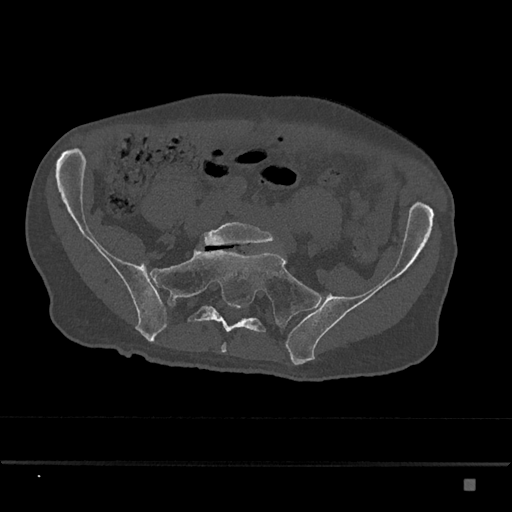
CT including the spine, one axial slice; slice 221 of 797 in the series (ordered by position); reconstruction kernel Br40s/3; bone window (W 1800 / L 400 HU); 0.5 mm slice thickness; 512 × 512 image matrix. Male patient, age 72 years. Case-level facts recorded for this patient, not image findings: primary cancer: prostate.
Outlined on this slice (semi-automatic segmentation, software-assisted and operator-edited):
- L5 vertebra: box from (x=203, y=222) to (x=274, y=246) px